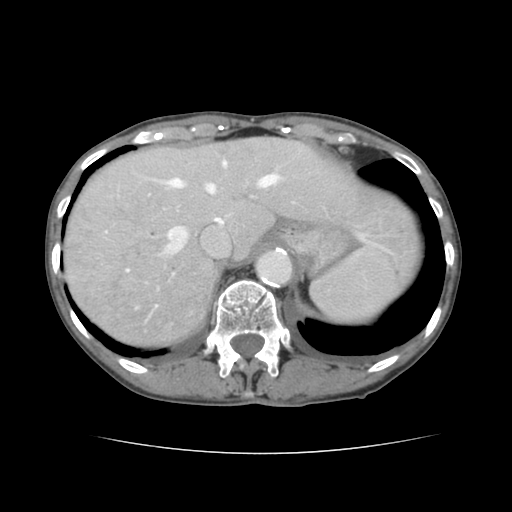
Contrast-enhanced abdominal CT, one axial slice; position 112 of 136 along the scan axis; soft-tissue window (W 400 / L 40 HU); 2.5 mm slice thickness; 512 × 512 image matrix, field of view 319 × 319 mm. Female patient, age 77 years. From the clinical record (not read from this slice): diagnosis: colorectal cancer liver metastases, imaged before liver resection; multiple liver metastases: yes; largest metastasis: 3 cm.
Annotated regions visible in this slice (manually delineated by an expert):
- hepatic veins: box from (x=139, y=161) to (x=278, y=259) px
- liver: (x=64, y=137)–(x=417, y=346)
- planned liver remnant (the part of the liver to remain after resection): (x=168, y=137)–(x=416, y=273)
- portal vein (with intrahepatic branches): (x=323, y=207)–(x=325, y=210)